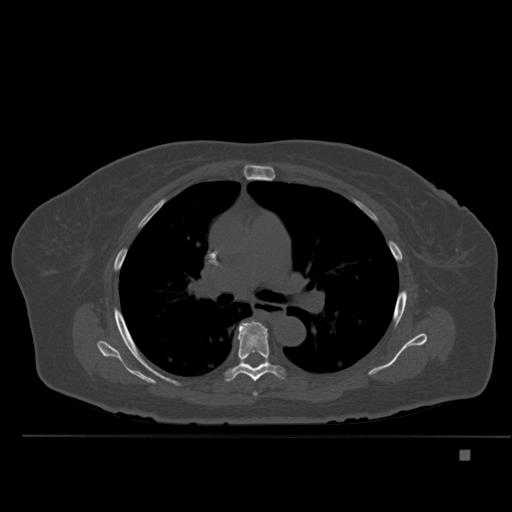
CT including the spine, one axial slice. Position 340 of 477 along the scan axis. Bone window (W 1800 / L 400 HU). 512 × 512 image matrix. Female patient, age 74 years. Case-level facts recorded for this patient, not image findings: primary cancer: colon.
Outlined on this slice (semi-automatically segmented with operator editing):
- T5 vertebra: bounding box [x1, y1, x2, y2] px = [253, 391, 257, 396]
- T6 vertebra: [226, 320, 284, 382]